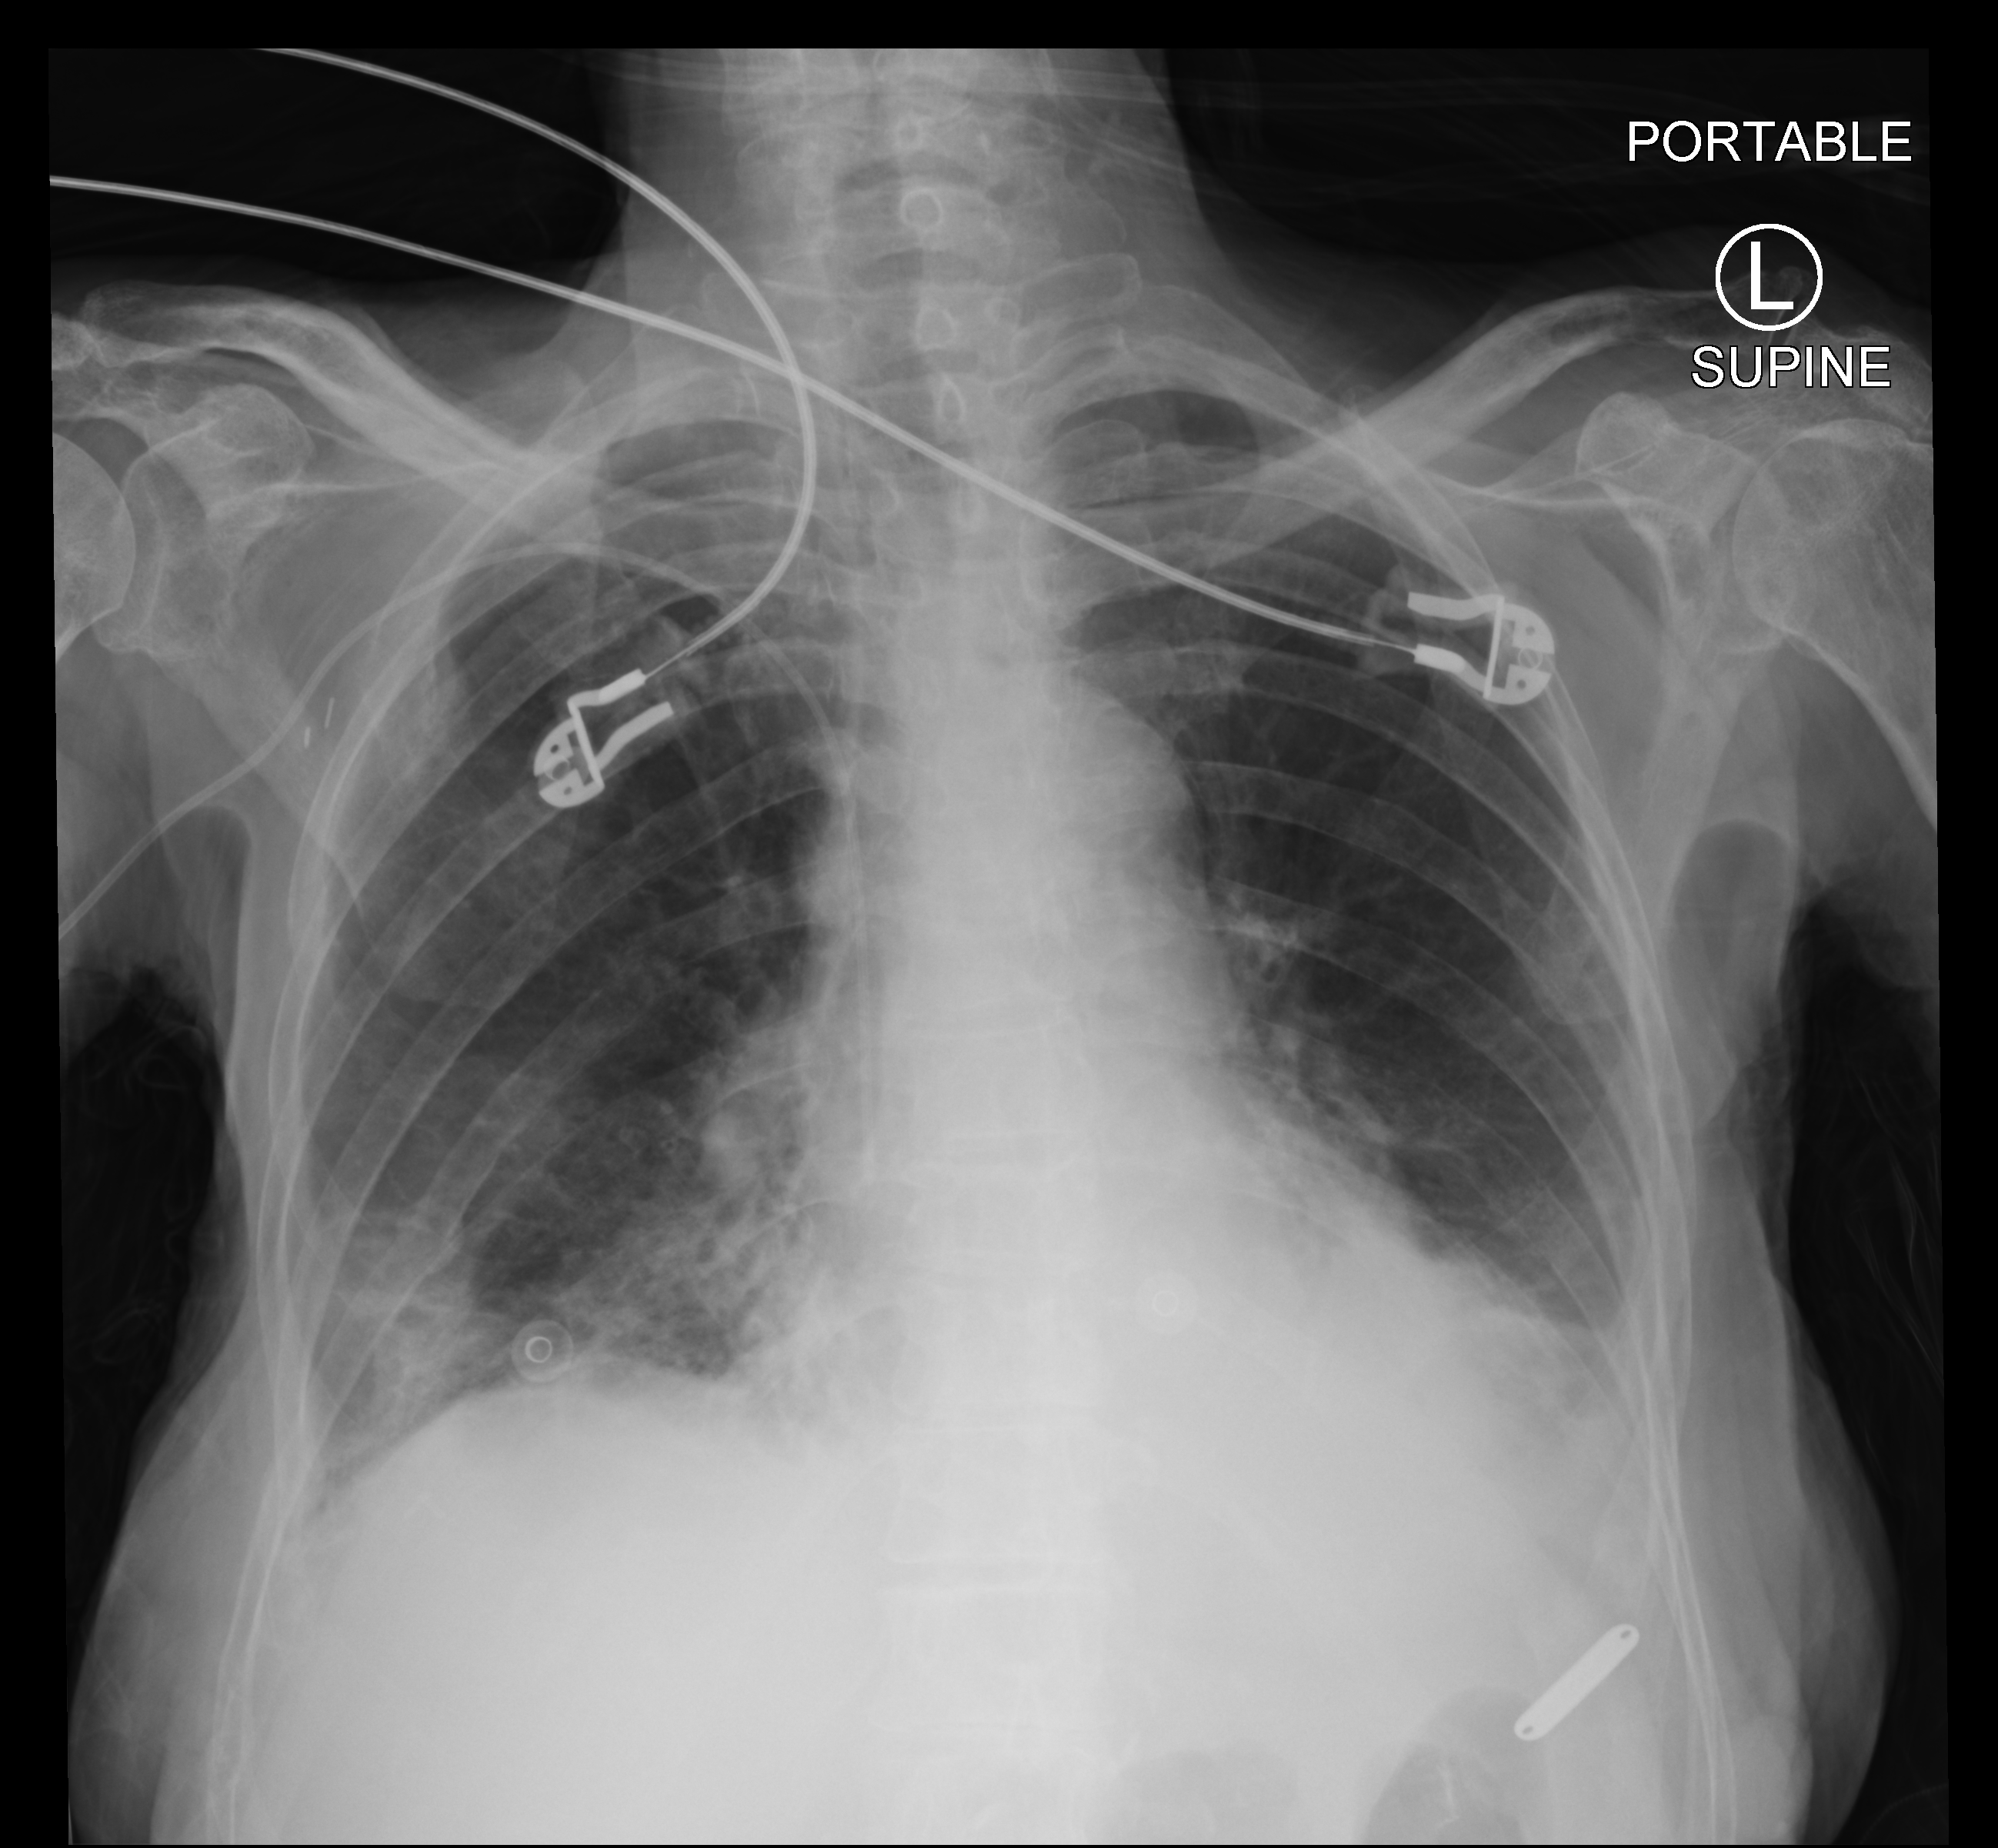
Portable chest radiograph, anteroposterior (AP) projection. Patient hospitalised with COVID-19; female, aged 60–74 years.
From the hospital-stay record, not from the radiograph (when in the stay this image was taken is not recorded):
- mechanically ventilated during this hospital stay: no
- admitted to intensive care during this hospital stay: no